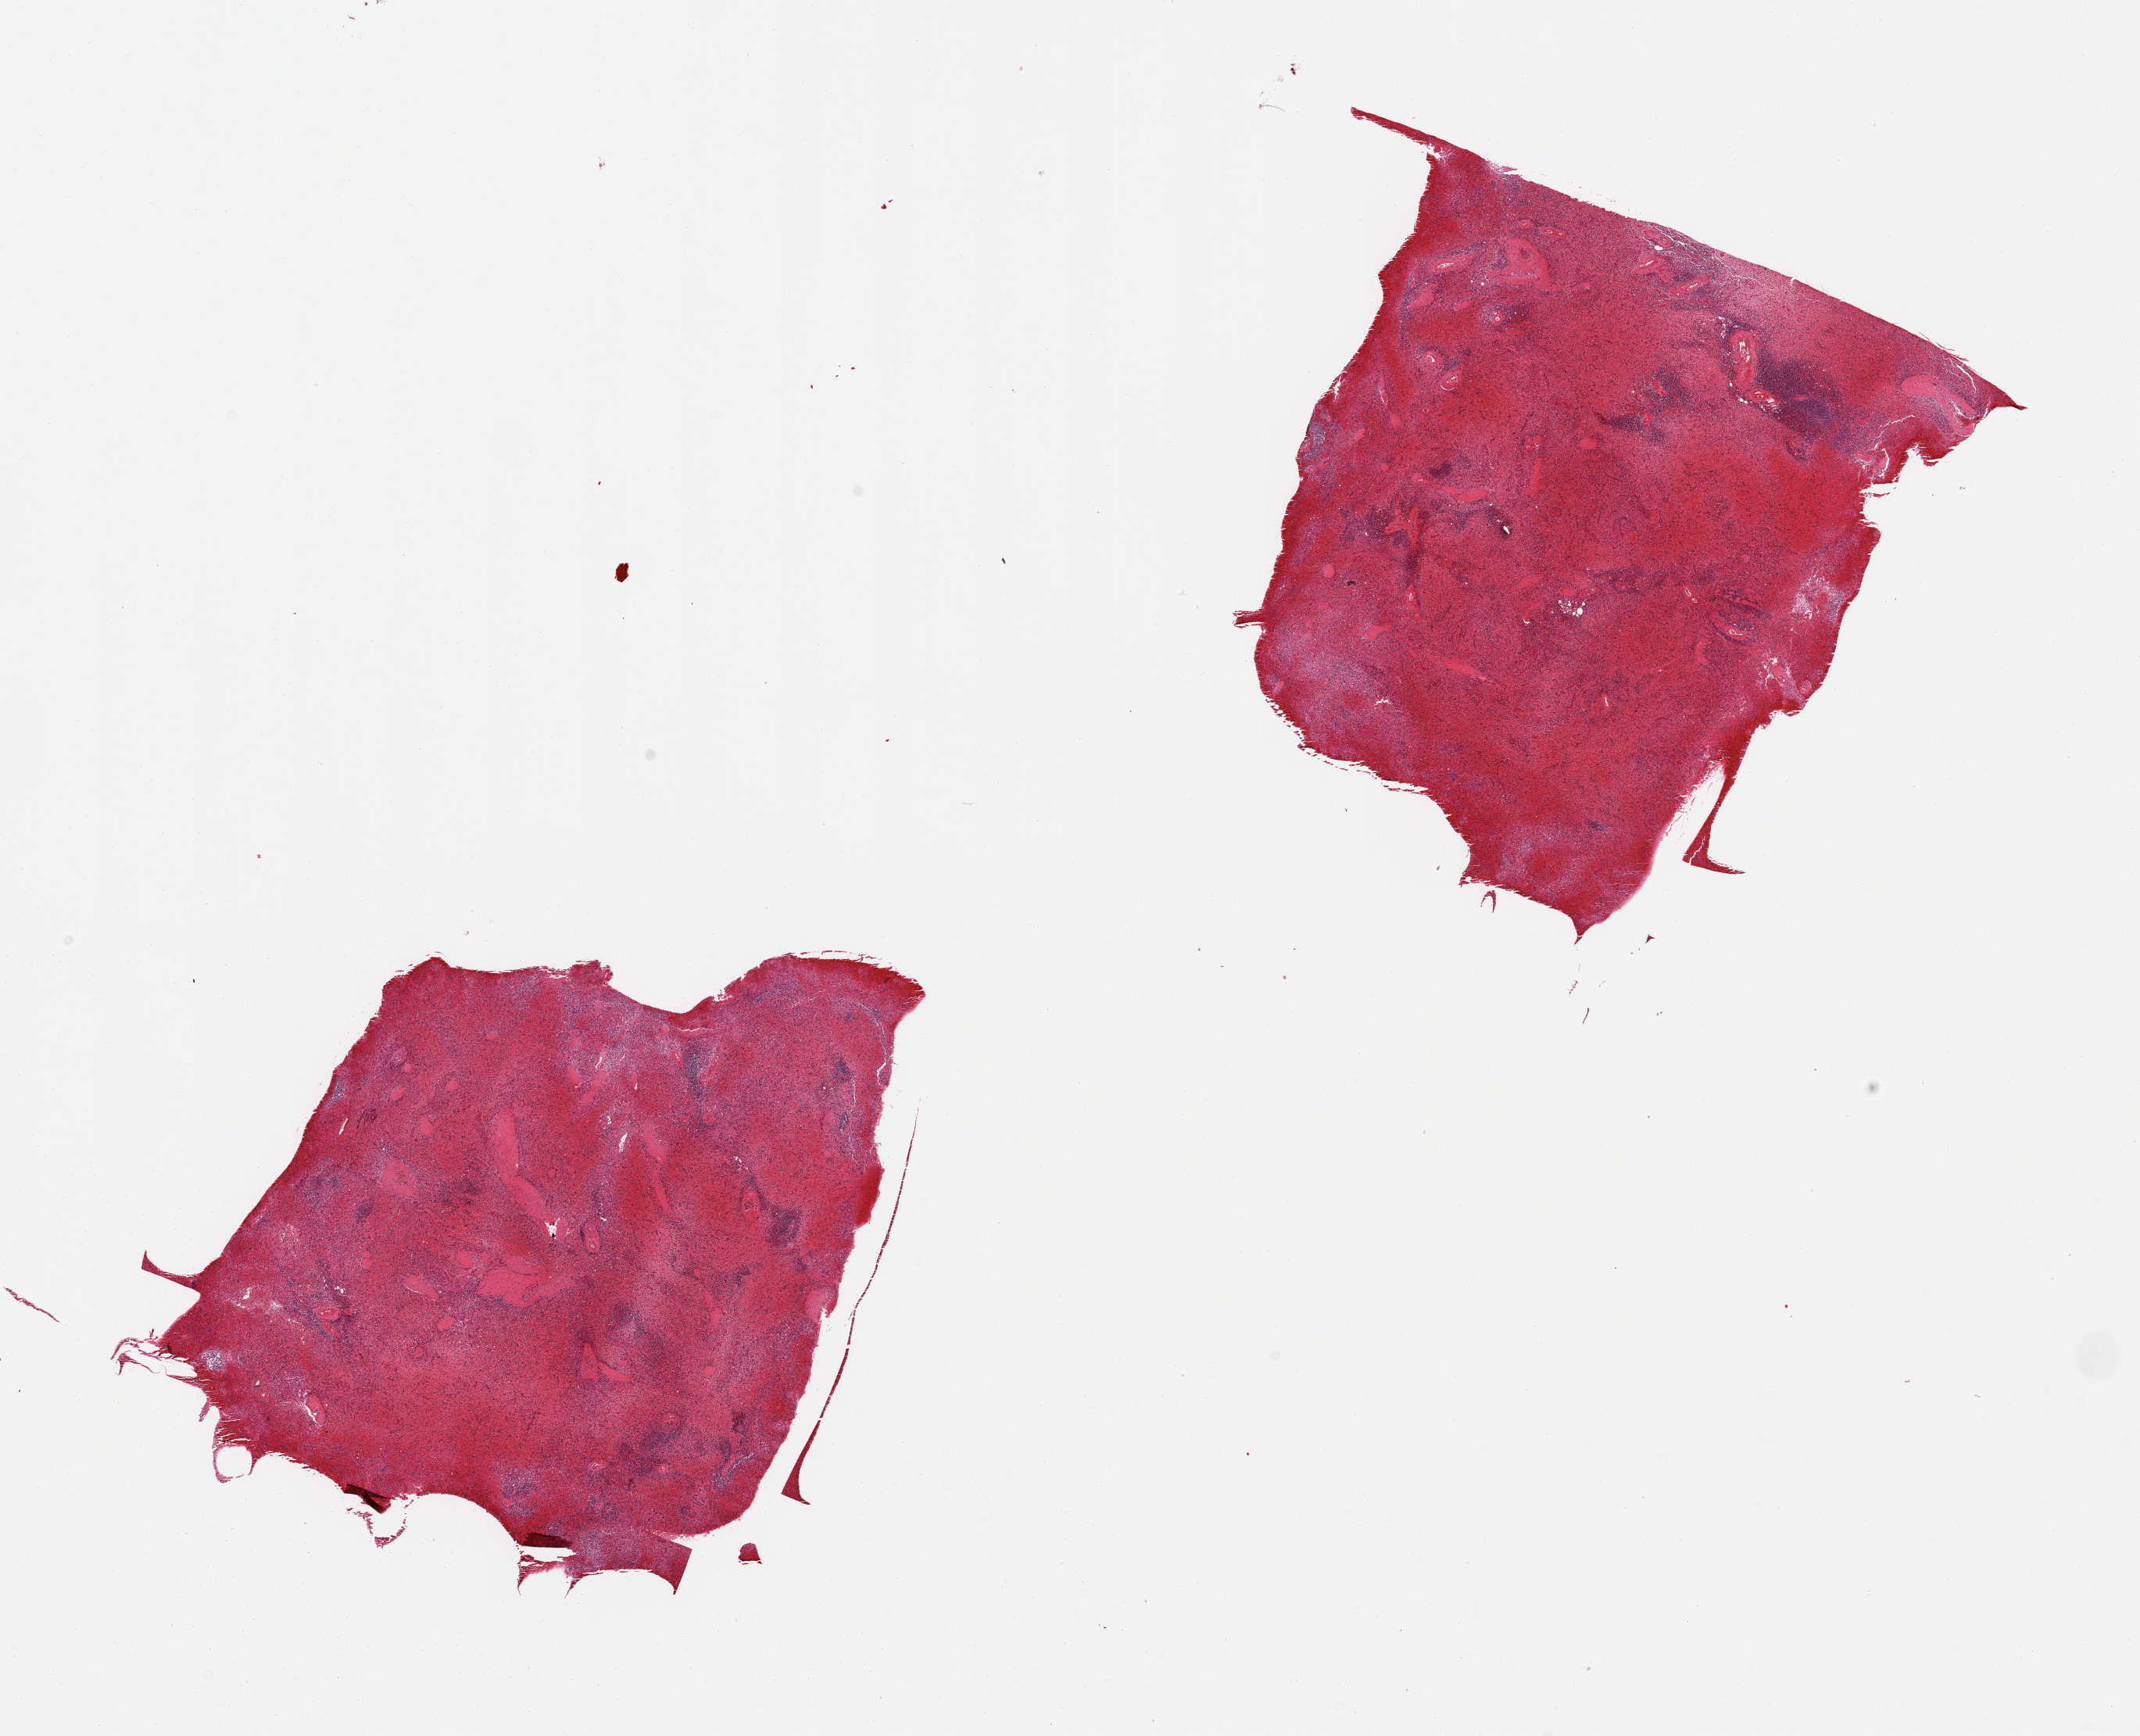
Whole-slide image, hematoxylin and eosin (H&E) stain, low-resolution overview of the scanned area, about 21.7 x 17.6 mm, PAXgene-fixed paraffin-embedded (PFPE) section, sampled site (target tissue): spleen, tissue donor sample.
* reviewer comment on this tissue sample: 2 pieces, marked congestion/autolysis